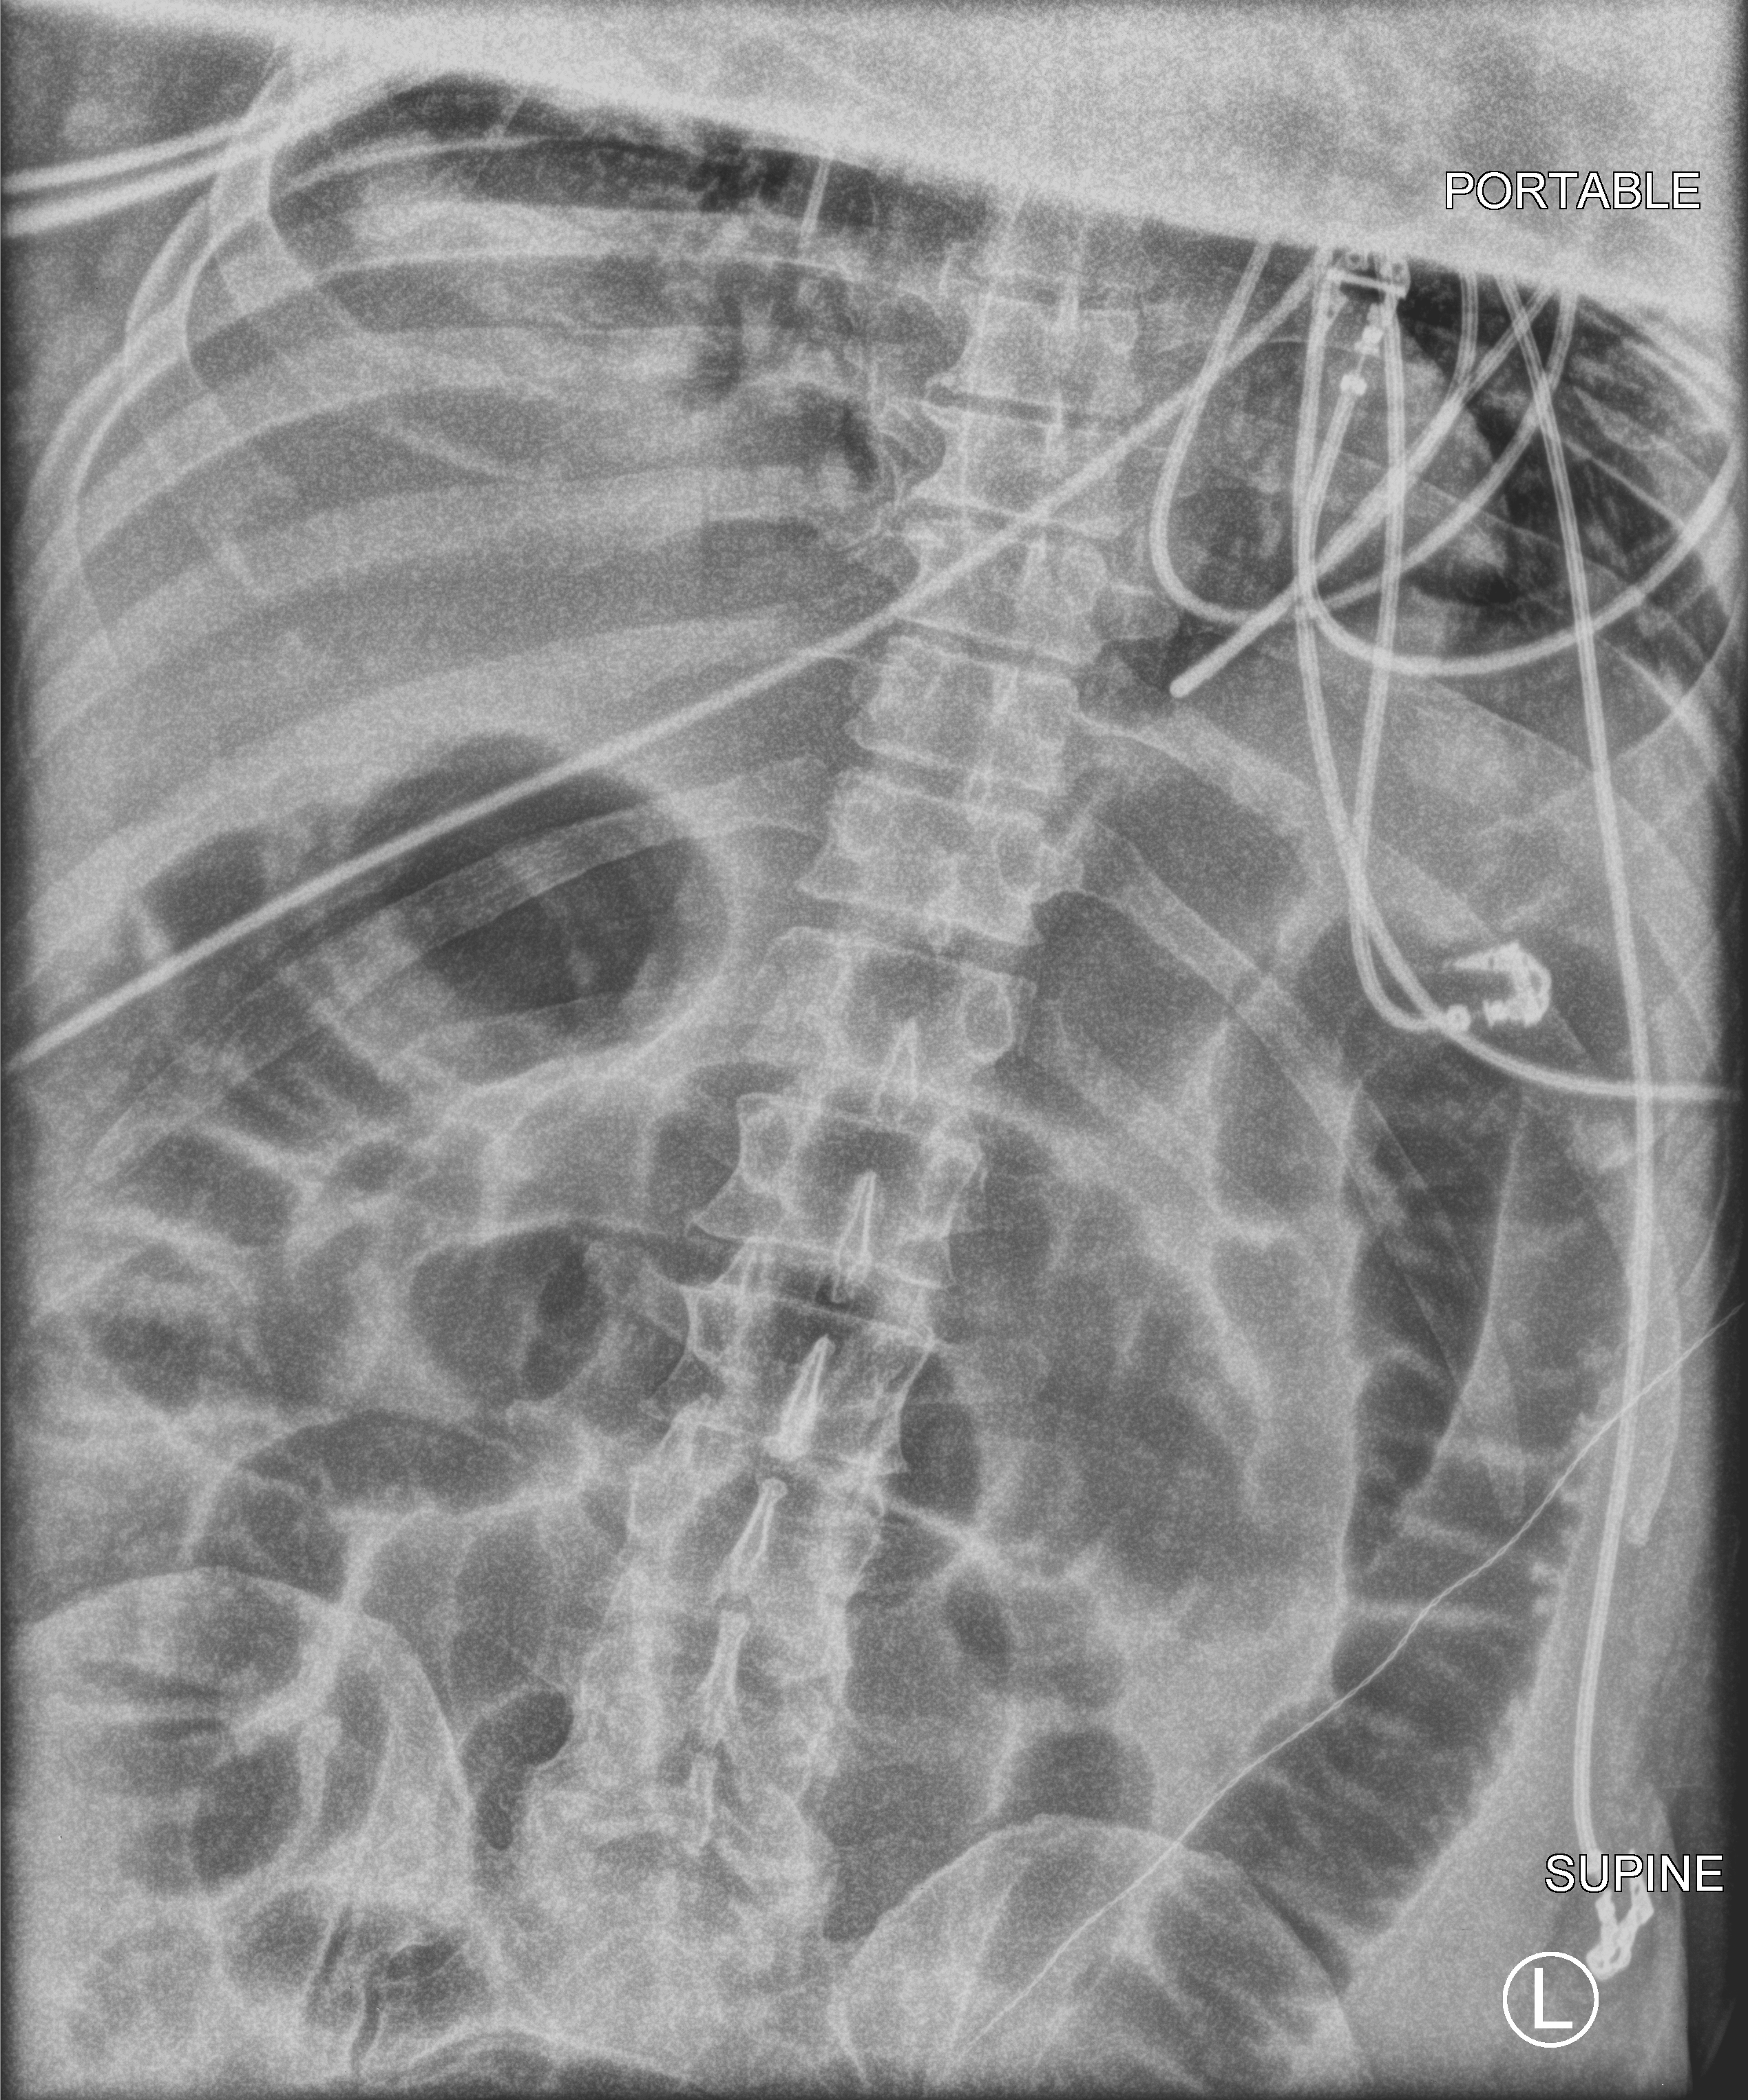
Bedside abdomen radiograph (computed radiography). Patient hospitalised with COVID-19; male, aged 18–59 years.
Admission-level facts for this patient (not findings on this image; timing relative to this image not recorded):
- length of hospital stay: 22 days
- diabetes (admission record): no